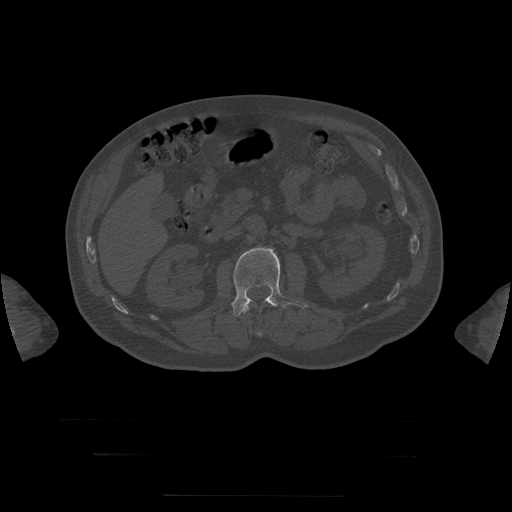
CT including the spine, one axial slice; position 27 of 397 along the scan axis; 120 kVp; bone window (W 1800 / L 400 HU); 1.25 mm slice thickness; 512 × 512 image matrix, field of view 510 × 510 mm. Patient age 73 years. Case-level facts recorded for this patient, not image findings: primary cancer: prostate.
Outlined on this slice (semi-automatic segmentation, software-assisted and operator-edited):
- L1 vertebra: bounding box (x1, y1, x2, y2) in pixels: (242, 301, 269, 336)